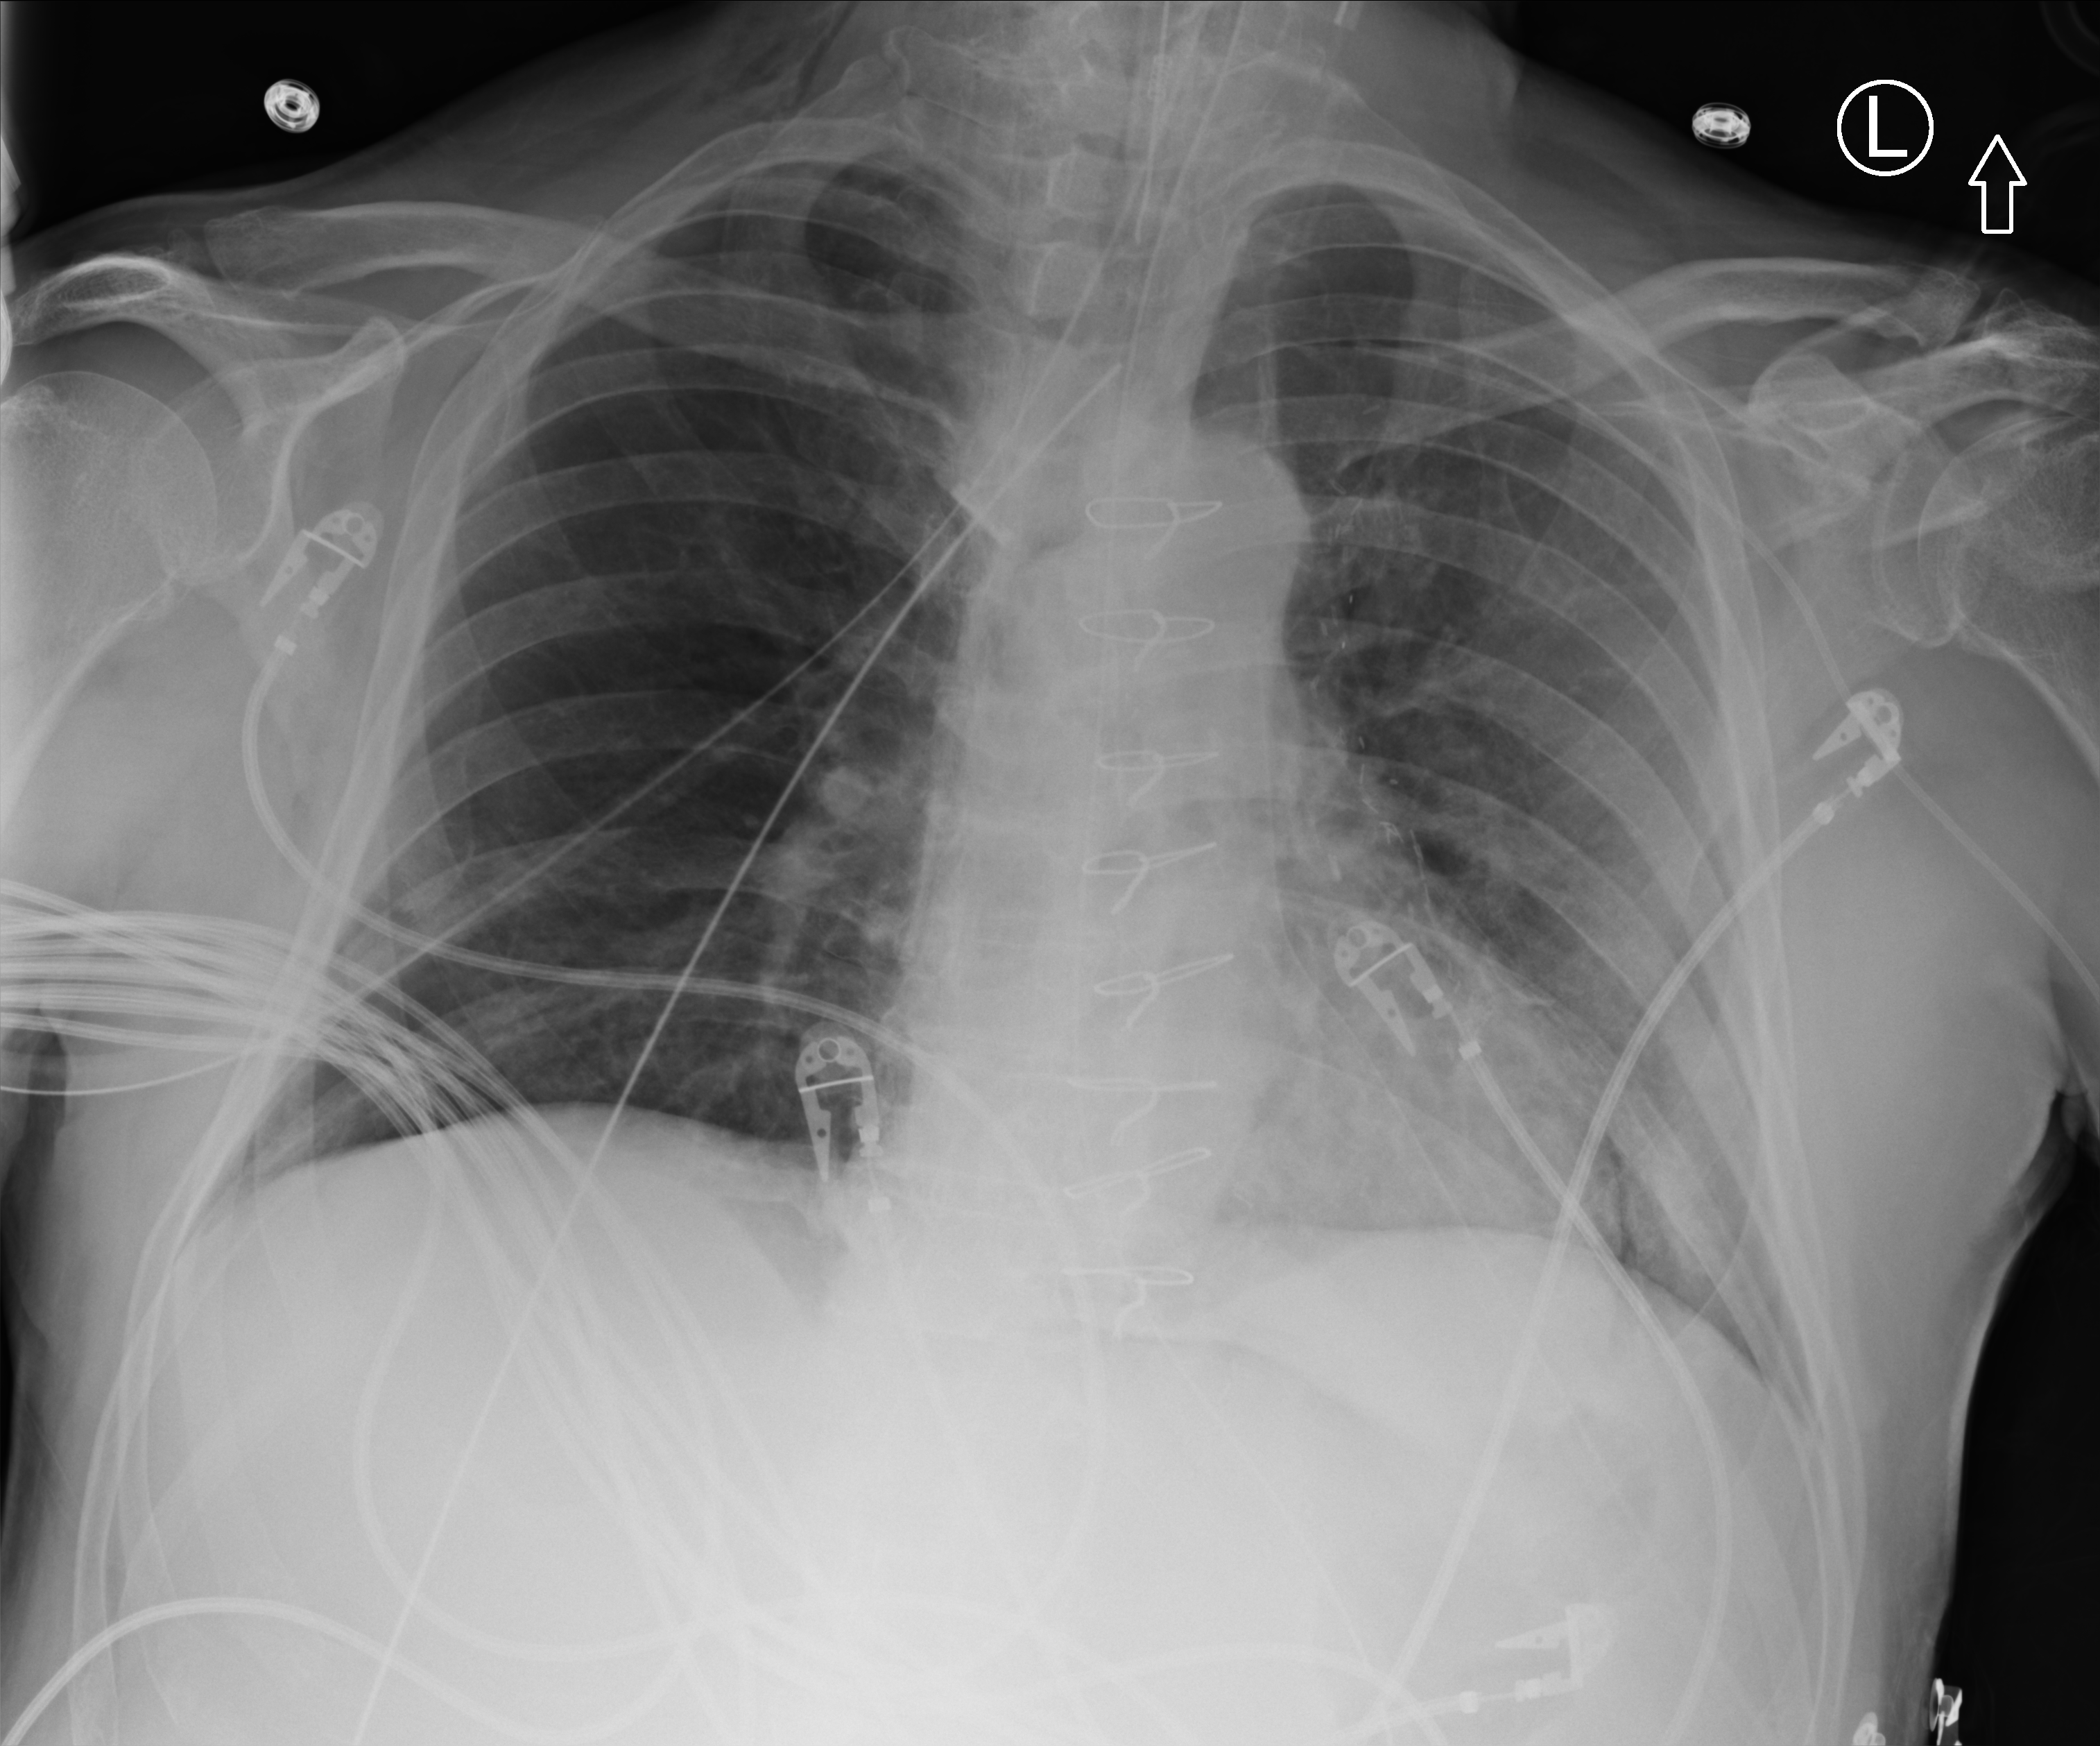
Bedside chest radiograph (computed radiography); anteroposterior (AP) projection. Patient hospitalised with COVID-19; male, aged 60–74 years.
From the hospital-stay record, not from the radiograph (when in the stay this image was taken is not recorded):
- mechanically ventilated during this hospital stay: yes
- admitted to intensive care during this hospital stay: yes
- hypertension (admission record): yes